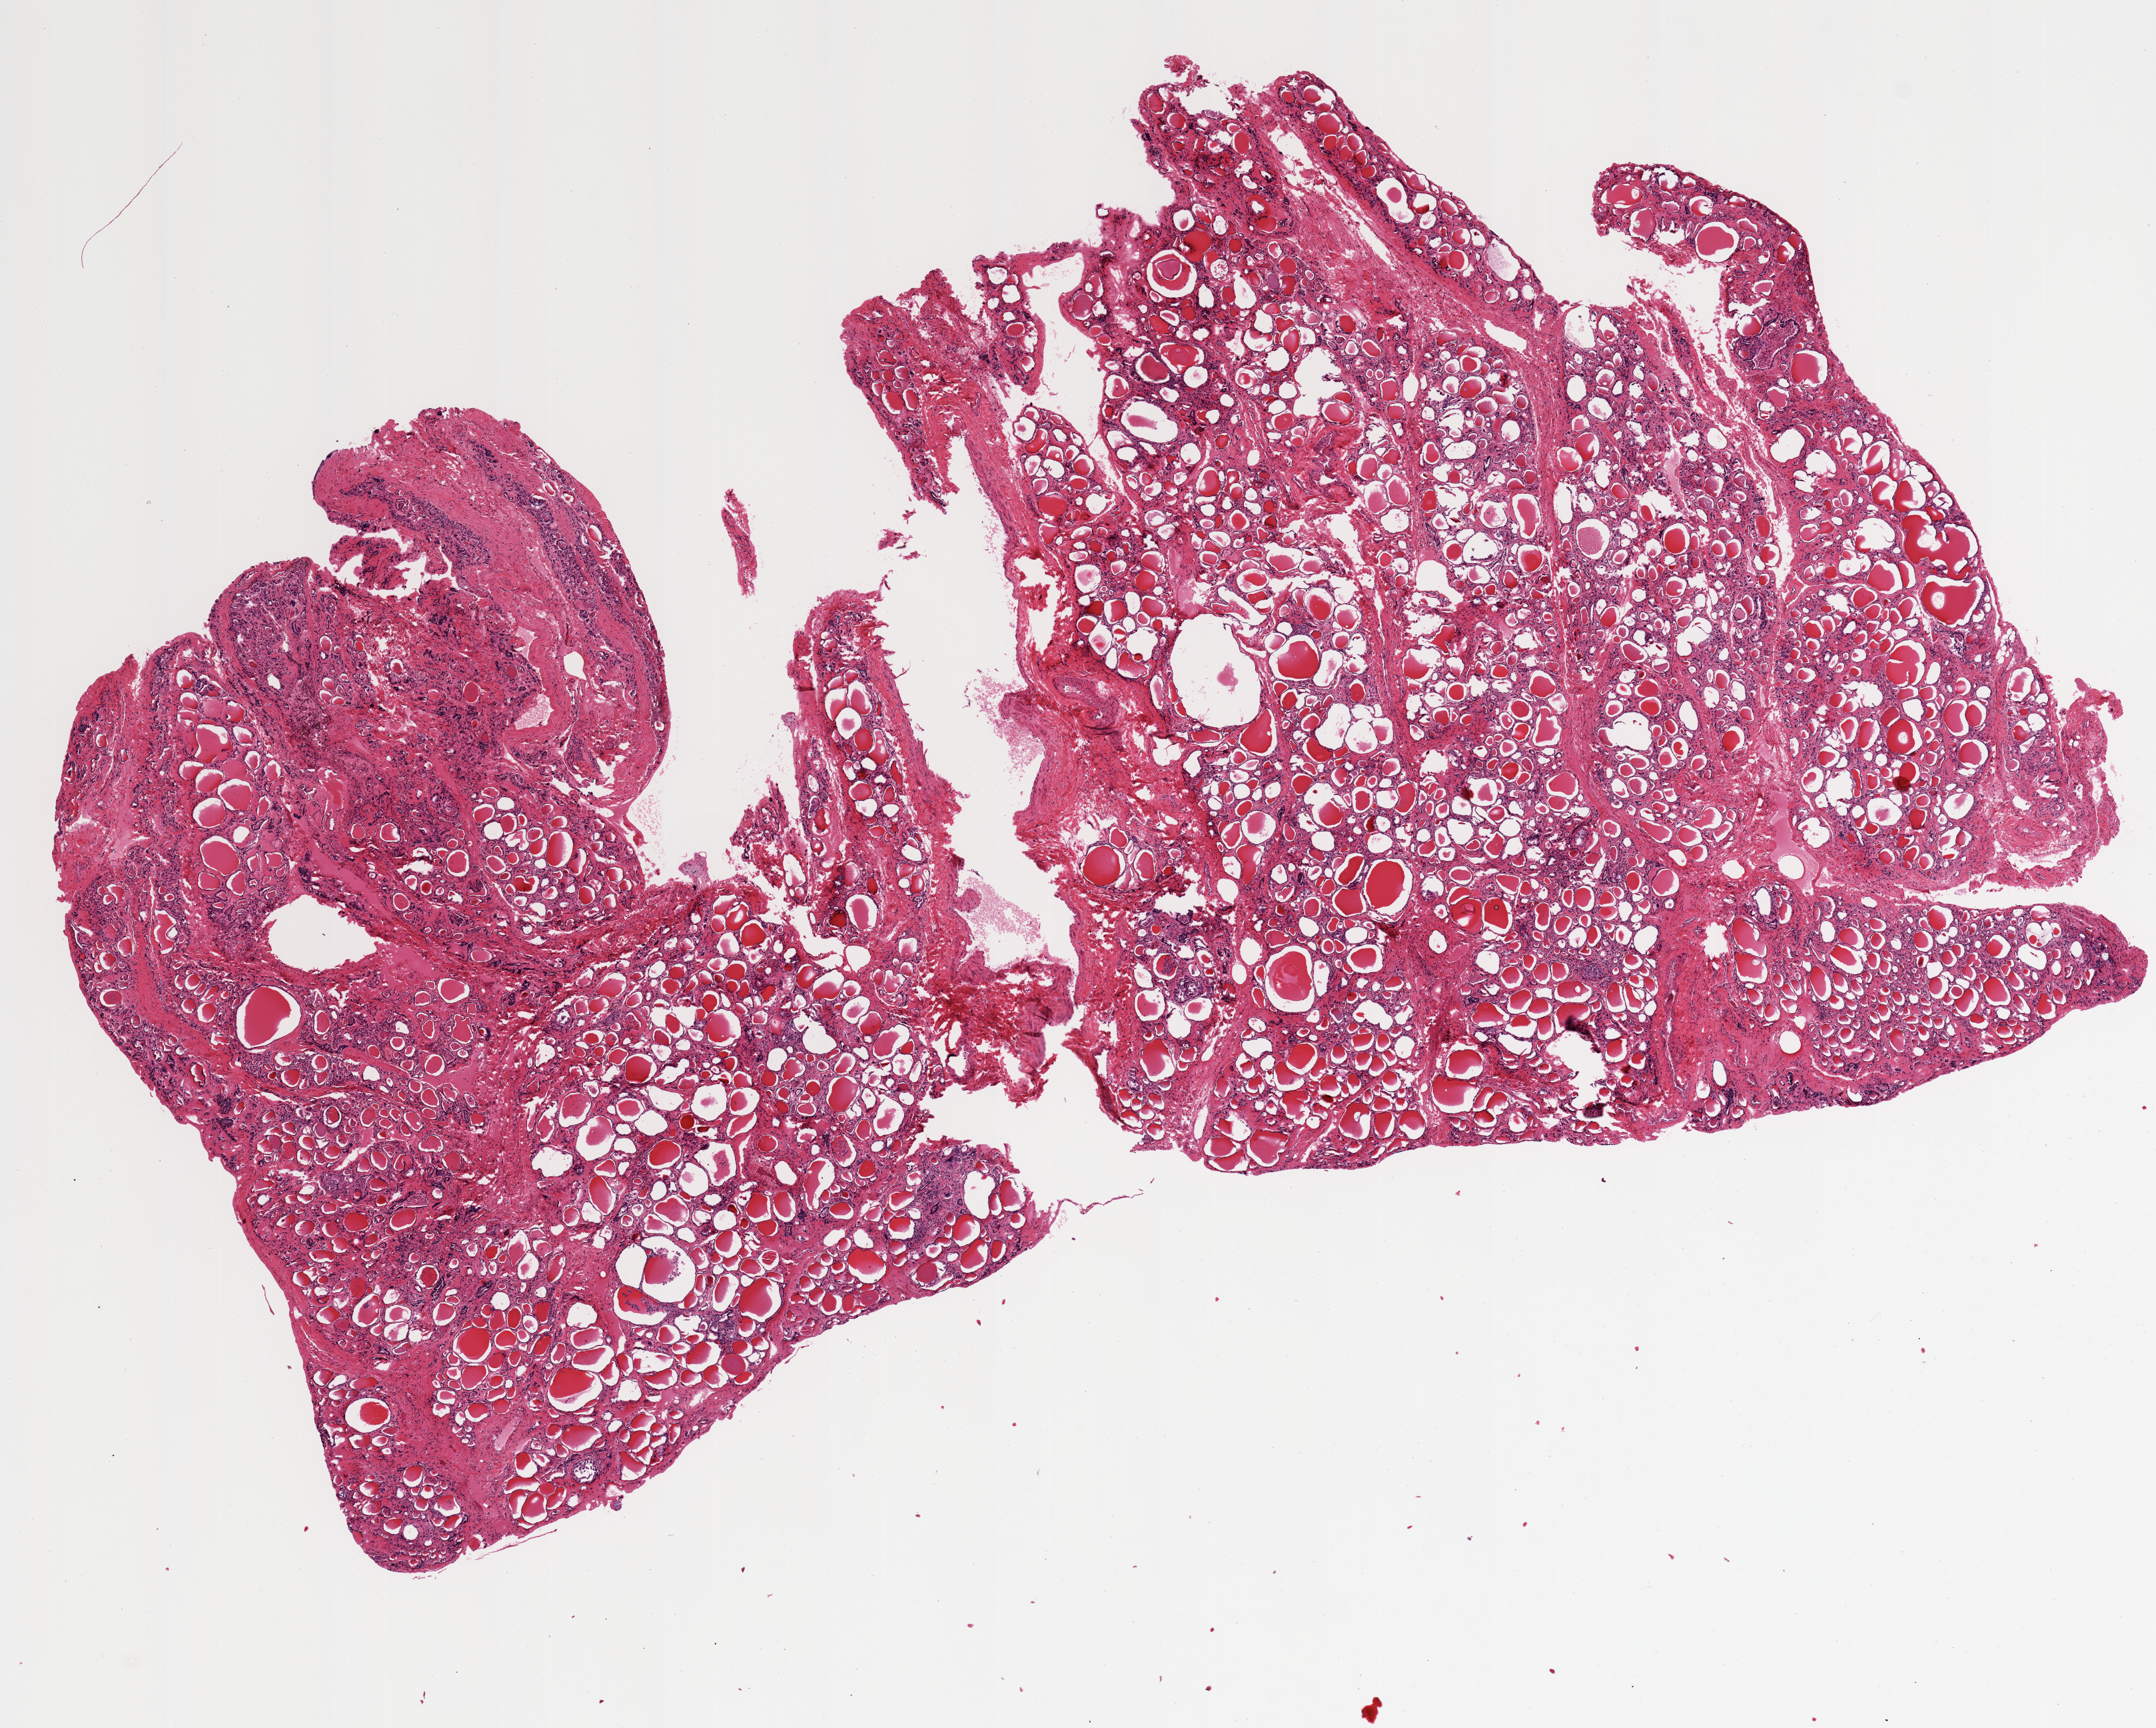
Whole-slide image, haematoxylin and eosin stain, brightfield — whole scanned area (about 12.8 x 10.3 mm) shown as a low-resolution overview, PAXgene-fixed paraffin-embedded (PFPE) section, sampled site (target tissue): thyroid, tissue donor sample.
- review note (as recorded): Regressive changes/fibrosis. ? late stage Hashimoto???s or medical thyroid suppression